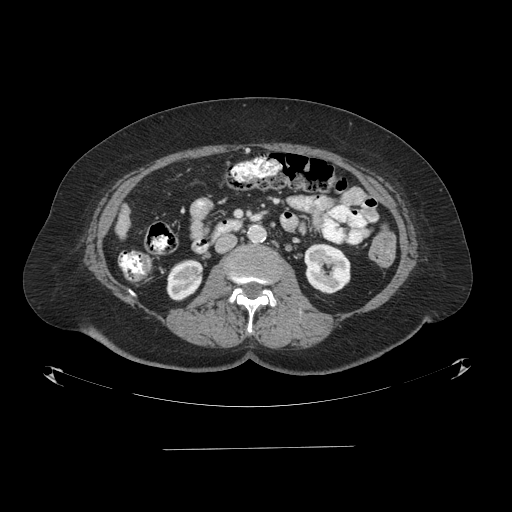
Contrast-enhanced abdominal CT (liver protocol), one axial slice; position 16 of 103 along the scan axis; one of 2 acquisitions stored at this slice position; soft-tissue window (W 400 / L 40 HU); 2.5 mm slice thickness; 512 × 512 image matrix. From the clinical record (not read from this slice): diagnosis: hepatocellular carcinoma (patient treated with transarterial chemoembolisation; whether this scan precedes or follows treatment is not stated here); TNM stage (as recorded): Stage-IIIA; Child-Pugh class: A; tumour nodularity: multinodular; tumour size: 5.2 cm.
Annotated regions visible in this slice (semi-automatically segmented with operator editing):
- liver parenchyma outside the tumour (the mass and vessels are separate outlines, so this box may not span the whole liver): bounding box <116,206,130,238> (left, top, right, bottom; pixels)